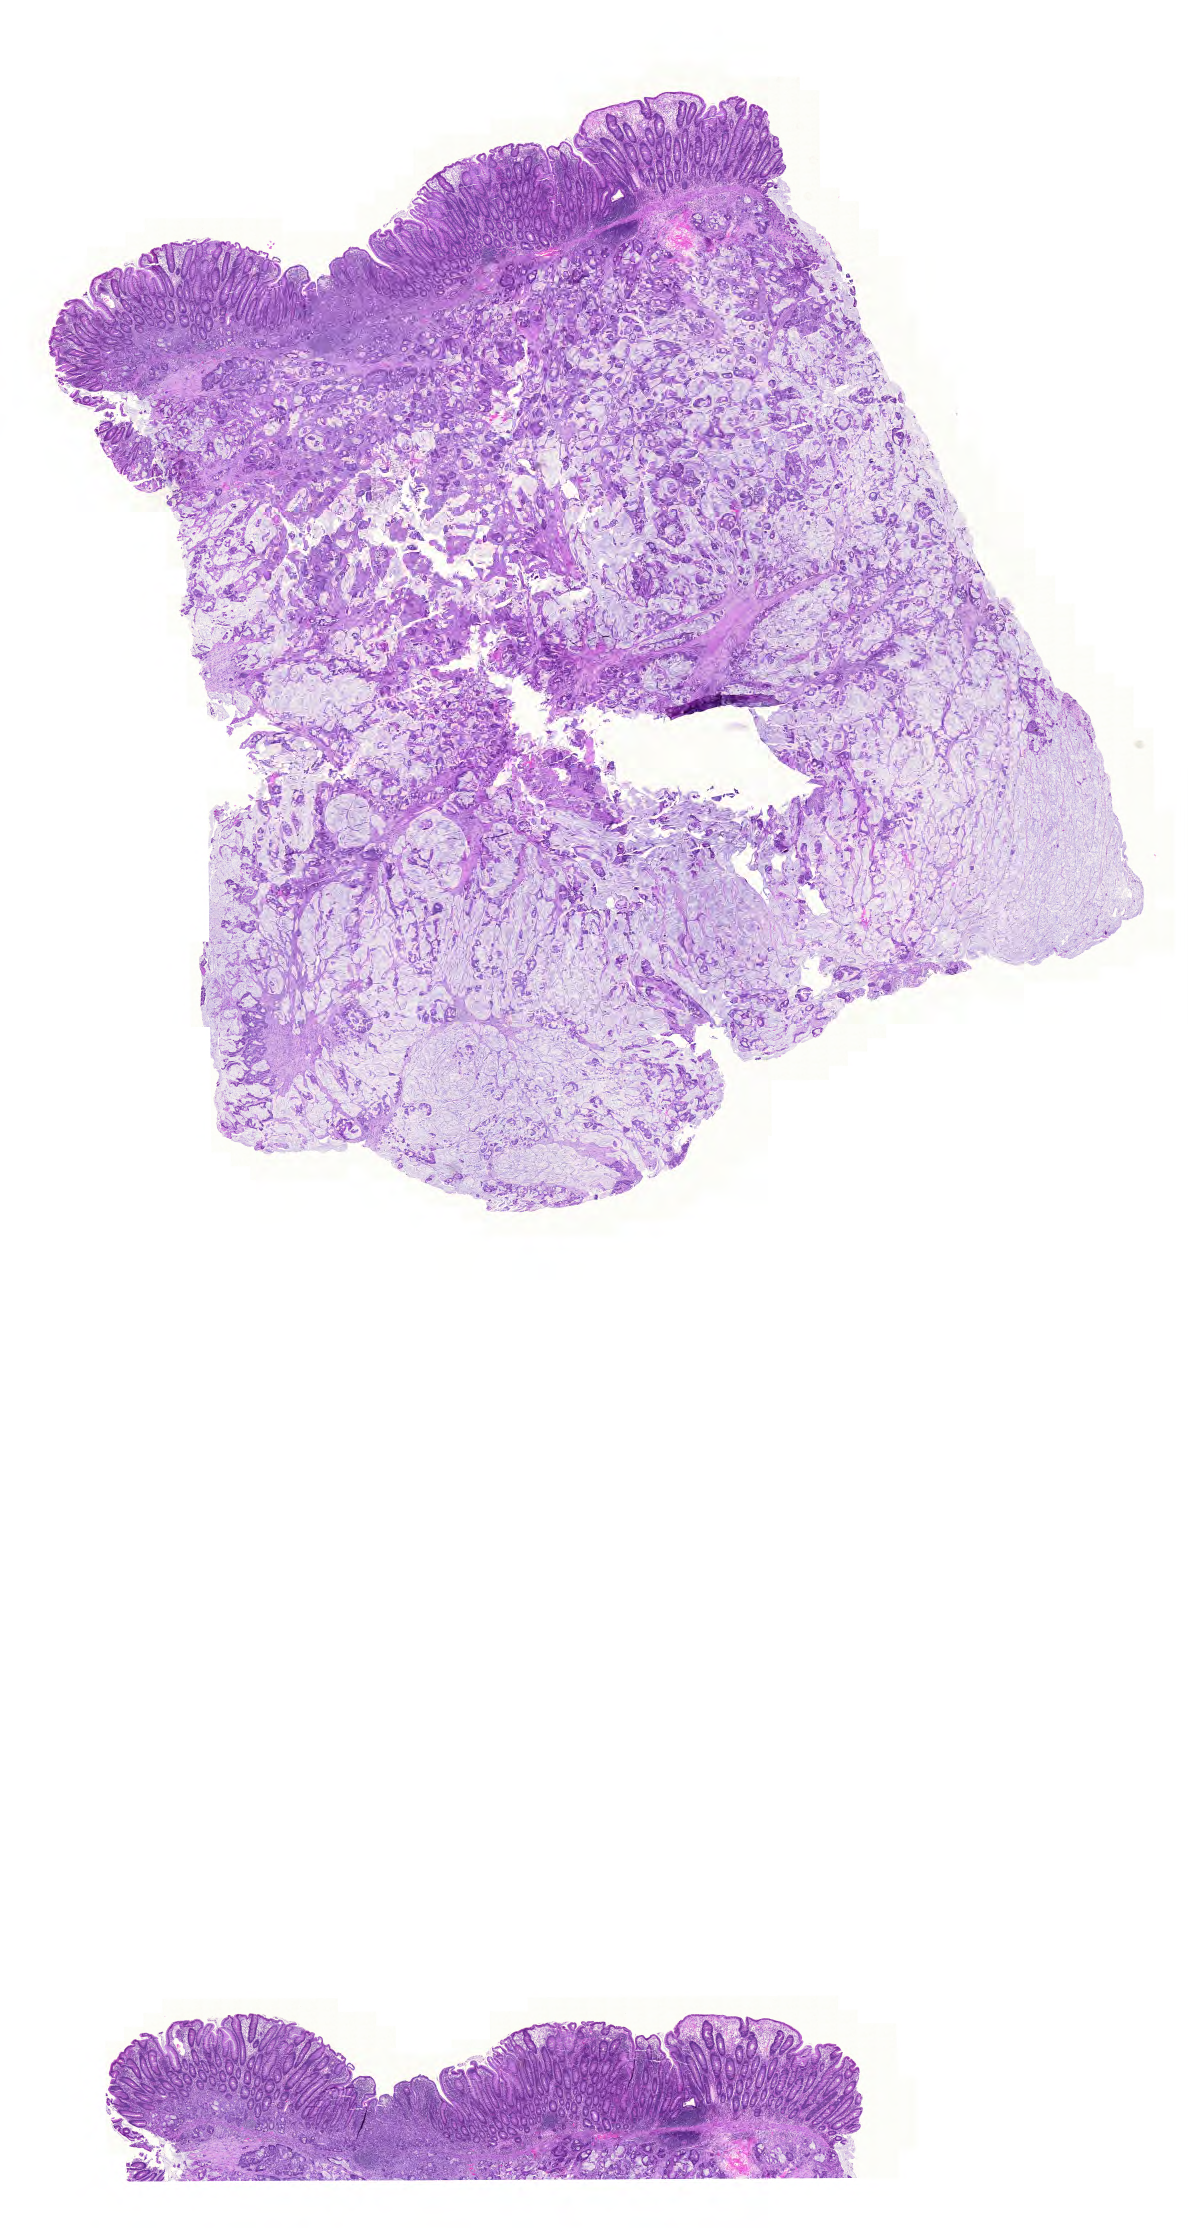
H&E-stained whole-slide image — whole scanned area (about 17.7 x 33.2 mm) shown as a low-resolution overview, formalin-fixed paraffin-embedded (FFPE) diagnostic section, colon, primary tumour sample. Female, age 64 years at initial diagnosis.
Histologic diagnosis: Mucinous adenocarcinoma. Lymph nodes positive (case pathology): 9 of 10 examined. AJCC pathologic stage: IV (5th edition).